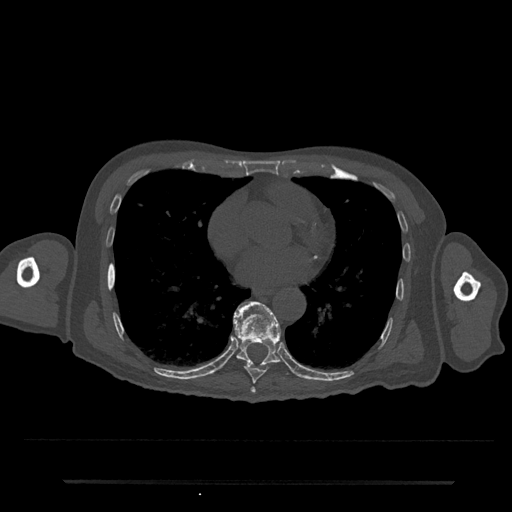
CT including the spine, one axial slice; position 395 of 797 along the scan axis; 120 kVp; bone window (W 1800 / L 400 HU); 512 × 512 image matrix, field of view 427 × 427 mm. Male patient, age 74 years. Case-level facts recorded for this patient, not image findings: primary cancer: prostate.
Annotated regions visible in this slice (semi-automatically segmented with operator editing):
- T7 vertebra: box from (x=250, y=387) to (x=256, y=394) px
- T8 vertebra: (x=244, y=362)–(x=265, y=384)
- T9 vertebra: (x=233, y=301)–(x=281, y=367)